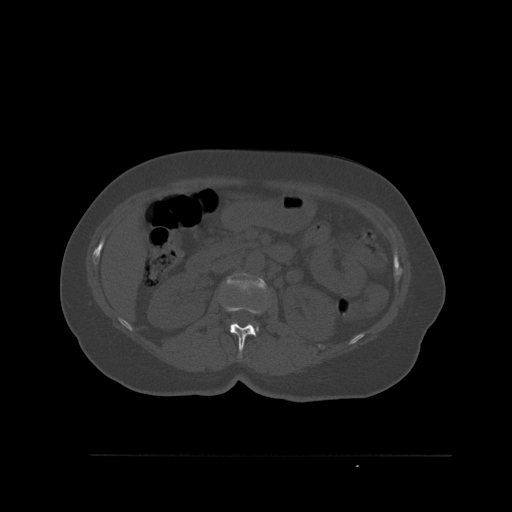
CT including the spine, one axial slice; position 259 of 527 along the scan axis; bone window (W 1800 / L 400 HU); 512 × 512 image matrix, field of view 470 × 470 mm. Patient: female, 73 years. Case-level facts recorded for this patient, not image findings: primary cancer: breast.
Outlined on this slice (semi-automatically segmented with operator editing):
- L1 vertebra: bounding box (x1, y1, x2, y2) in pixels: (223, 305, 265, 358)
- L2 vertebra: (227, 273, 265, 330)